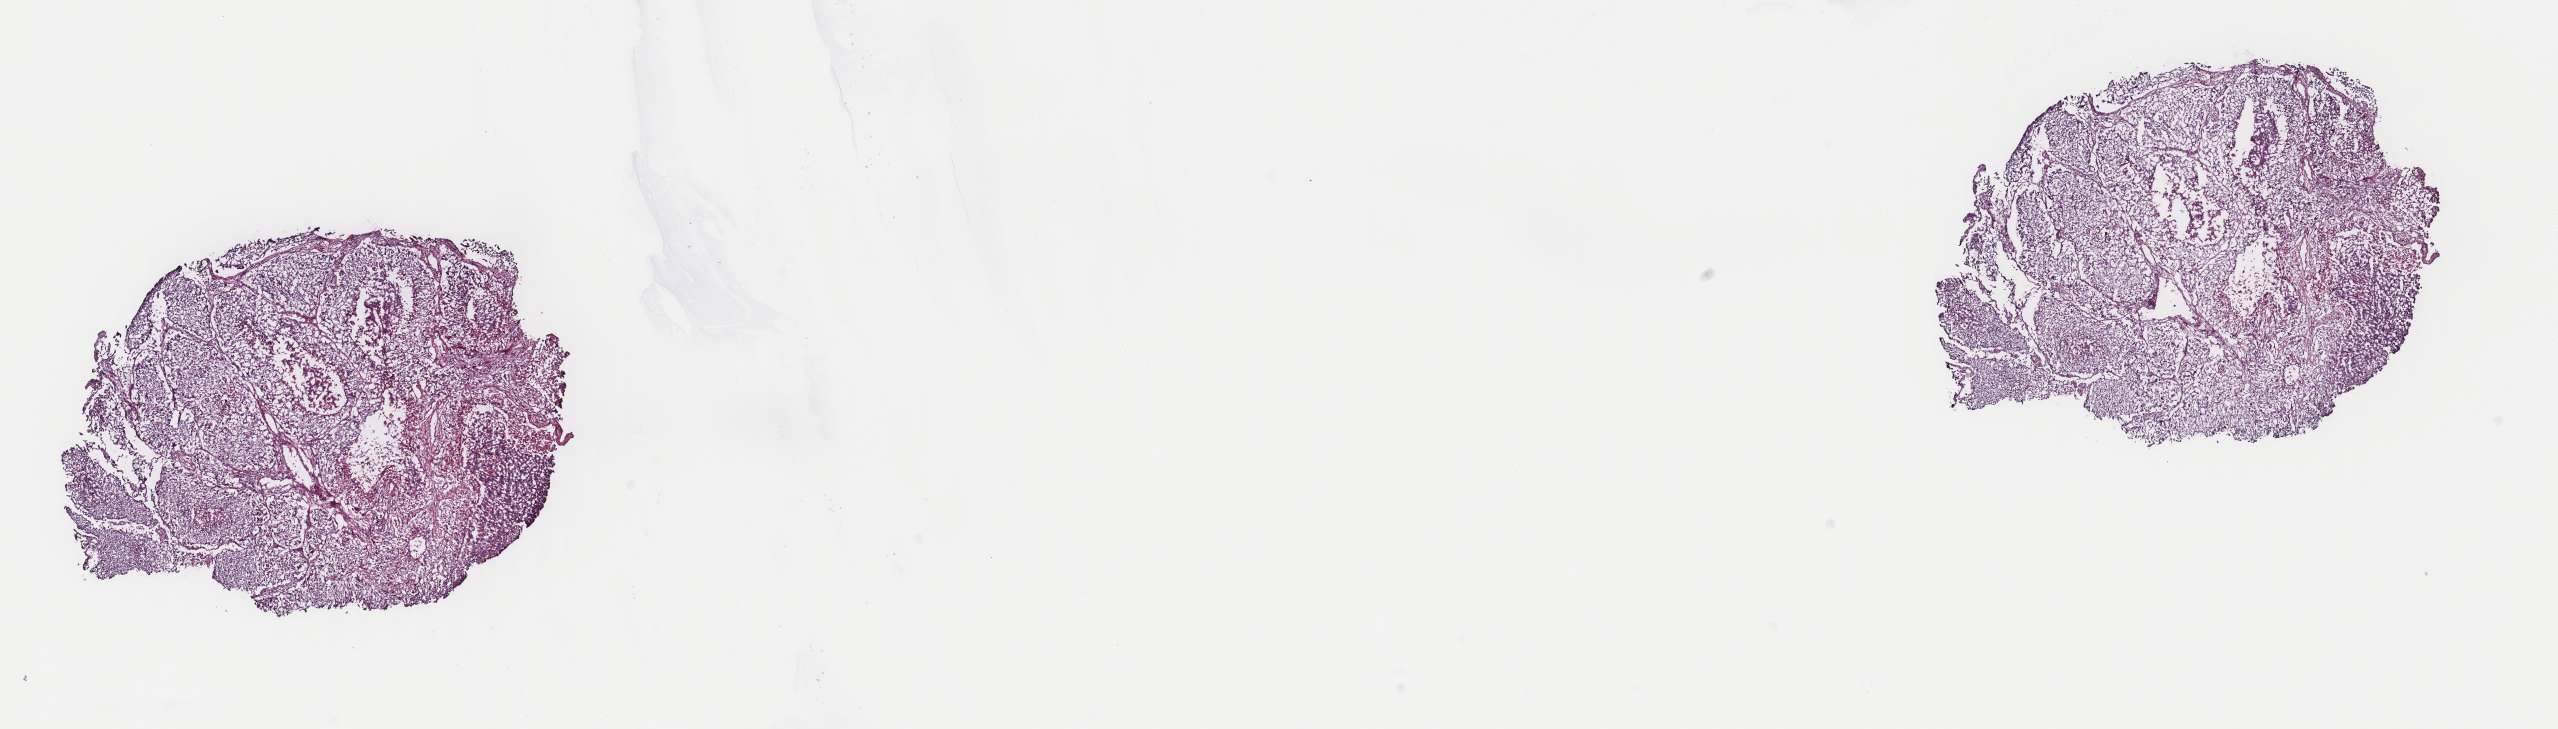
Whole-slide histology image, Hematoxylin and eosin (H&E) stained, a low-resolution overview of the entire scanned area, about 20.3 x 5.8 mm (acquisition: 40x scan), frozen section, primary tumour sample from the lung. Patient: male, age at initial diagnosis 70 years. Slide review estimates, as recorded: tumour cells 85%, tumour nuclei 95%, normal cells 0%, stromal cells 10%, necrosis 5%. Inflammatory infiltration, as recorded: lymphocyte infiltration 2%, monocyte infiltration 2%, neutrophil infiltration 0%.
Laterality: left. Histologic diagnosis: Squamous cell carcinoma, NOS (lower lobe, lung). AJCC pathologic stage: IA (6th edition).